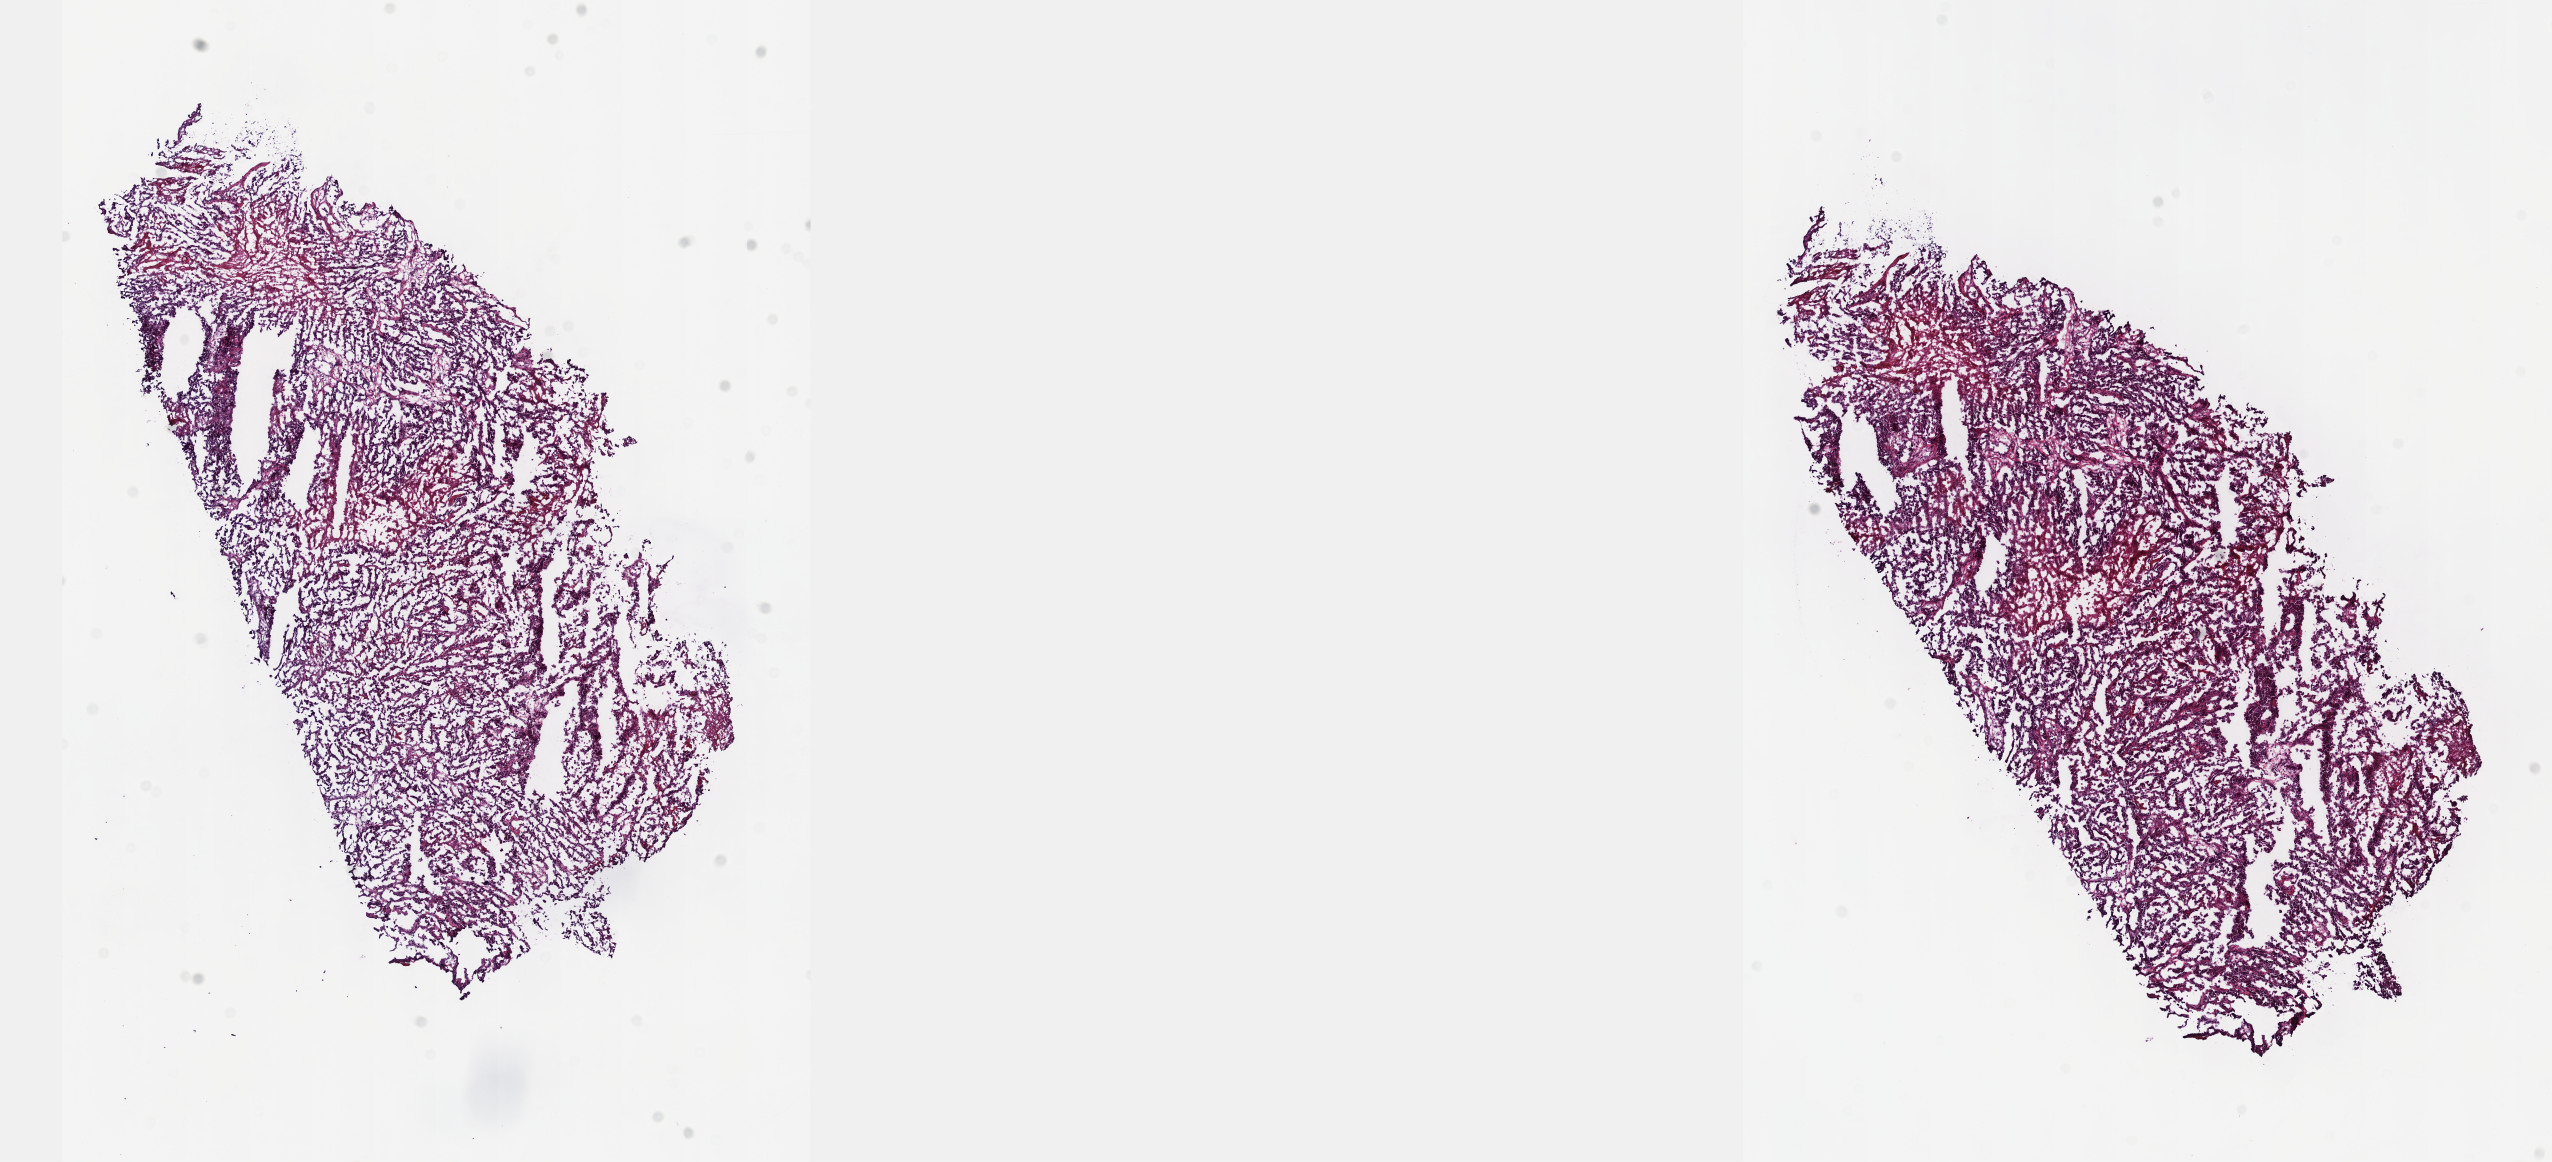
Whole-slide histology image, H&E-stained — a low-resolution overview of the entire scanned area, about 20.6 x 9.4 mm (from a 40x scan); frozen section from the top of the tissue portion; mesothelium, primary tumour sample. Male patient; age at initial diagnosis 46 years. Composition of this section per pathologist review: tumour cells 85%, tumour nuclei 70%, normal cells 0%, stromal cells 0%, necrosis 15%. Inflammatory infiltration, as recorded: lymphocyte infiltration 2%, monocyte infiltration 0%, neutrophil infiltration 0%.
Pathologic diagnosis: Epithelioid mesothelioma, malignant (pleura, NOS). AJCC pathologic stage: II. Laterality: left.